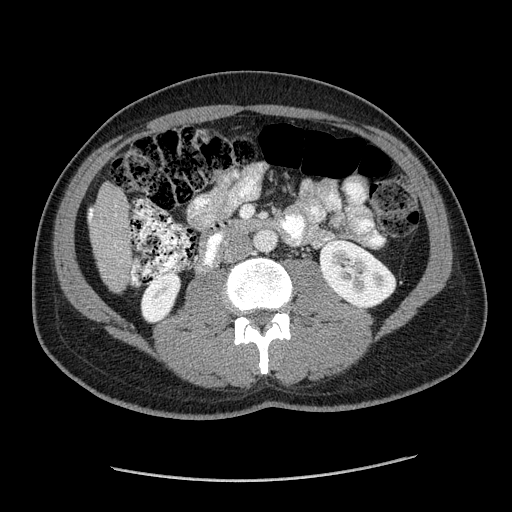
Contrast-enhanced abdominal CT (liver protocol), one axial slice; position 37 of 182 along the scan axis; 120 kVp; soft-tissue window (W 400 / L 40 HU); 2.5 mm slice thickness; 512 × 512 image matrix. From the clinical record (not read from this slice): diagnosis: hepatocellular carcinoma (patient treated with transarterial chemoembolisation; whether this scan precedes or follows treatment is not stated here); TNM stage (as recorded): Stage-I; Child-Pugh class: A; tumour differentiation: well differentiated; tumour size: 3.1 cm.
Outlined on this slice (semi-automatically segmented with operator editing):
- liver parenchyma outside the tumour (the mass and vessels are separate outlines, so this box may not span the whole liver): bounding box <88,182,132,290> (left, top, right, bottom; pixels)
- liver vessels: <89,210,93,220>